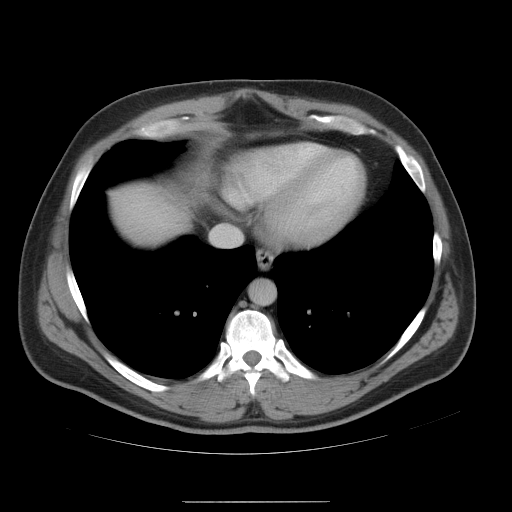
Contrast-enhanced abdominal CT, one axial slice; position 48 of 54 along the scan axis; 120 kVp; intravenous contrast given; soft-tissue window (W 400 / L 40 HU); 5 mm slice thickness; 512 × 512 image matrix, field of view 436 × 436 mm. Male patient, age 40 years. Case-level facts recorded for this patient, not image findings: diagnosis: colorectal cancer liver metastases, imaged before liver resection; multiple liver metastases: no; largest metastasis: 15 cm; disease in both lobes: no.
Annotated regions visible in this slice (manually delineated by an expert):
- hepatic veins: bounding box (x1, y1, x2, y2) in pixels: (213, 229, 240, 245)
- liver: (108, 180, 194, 247)